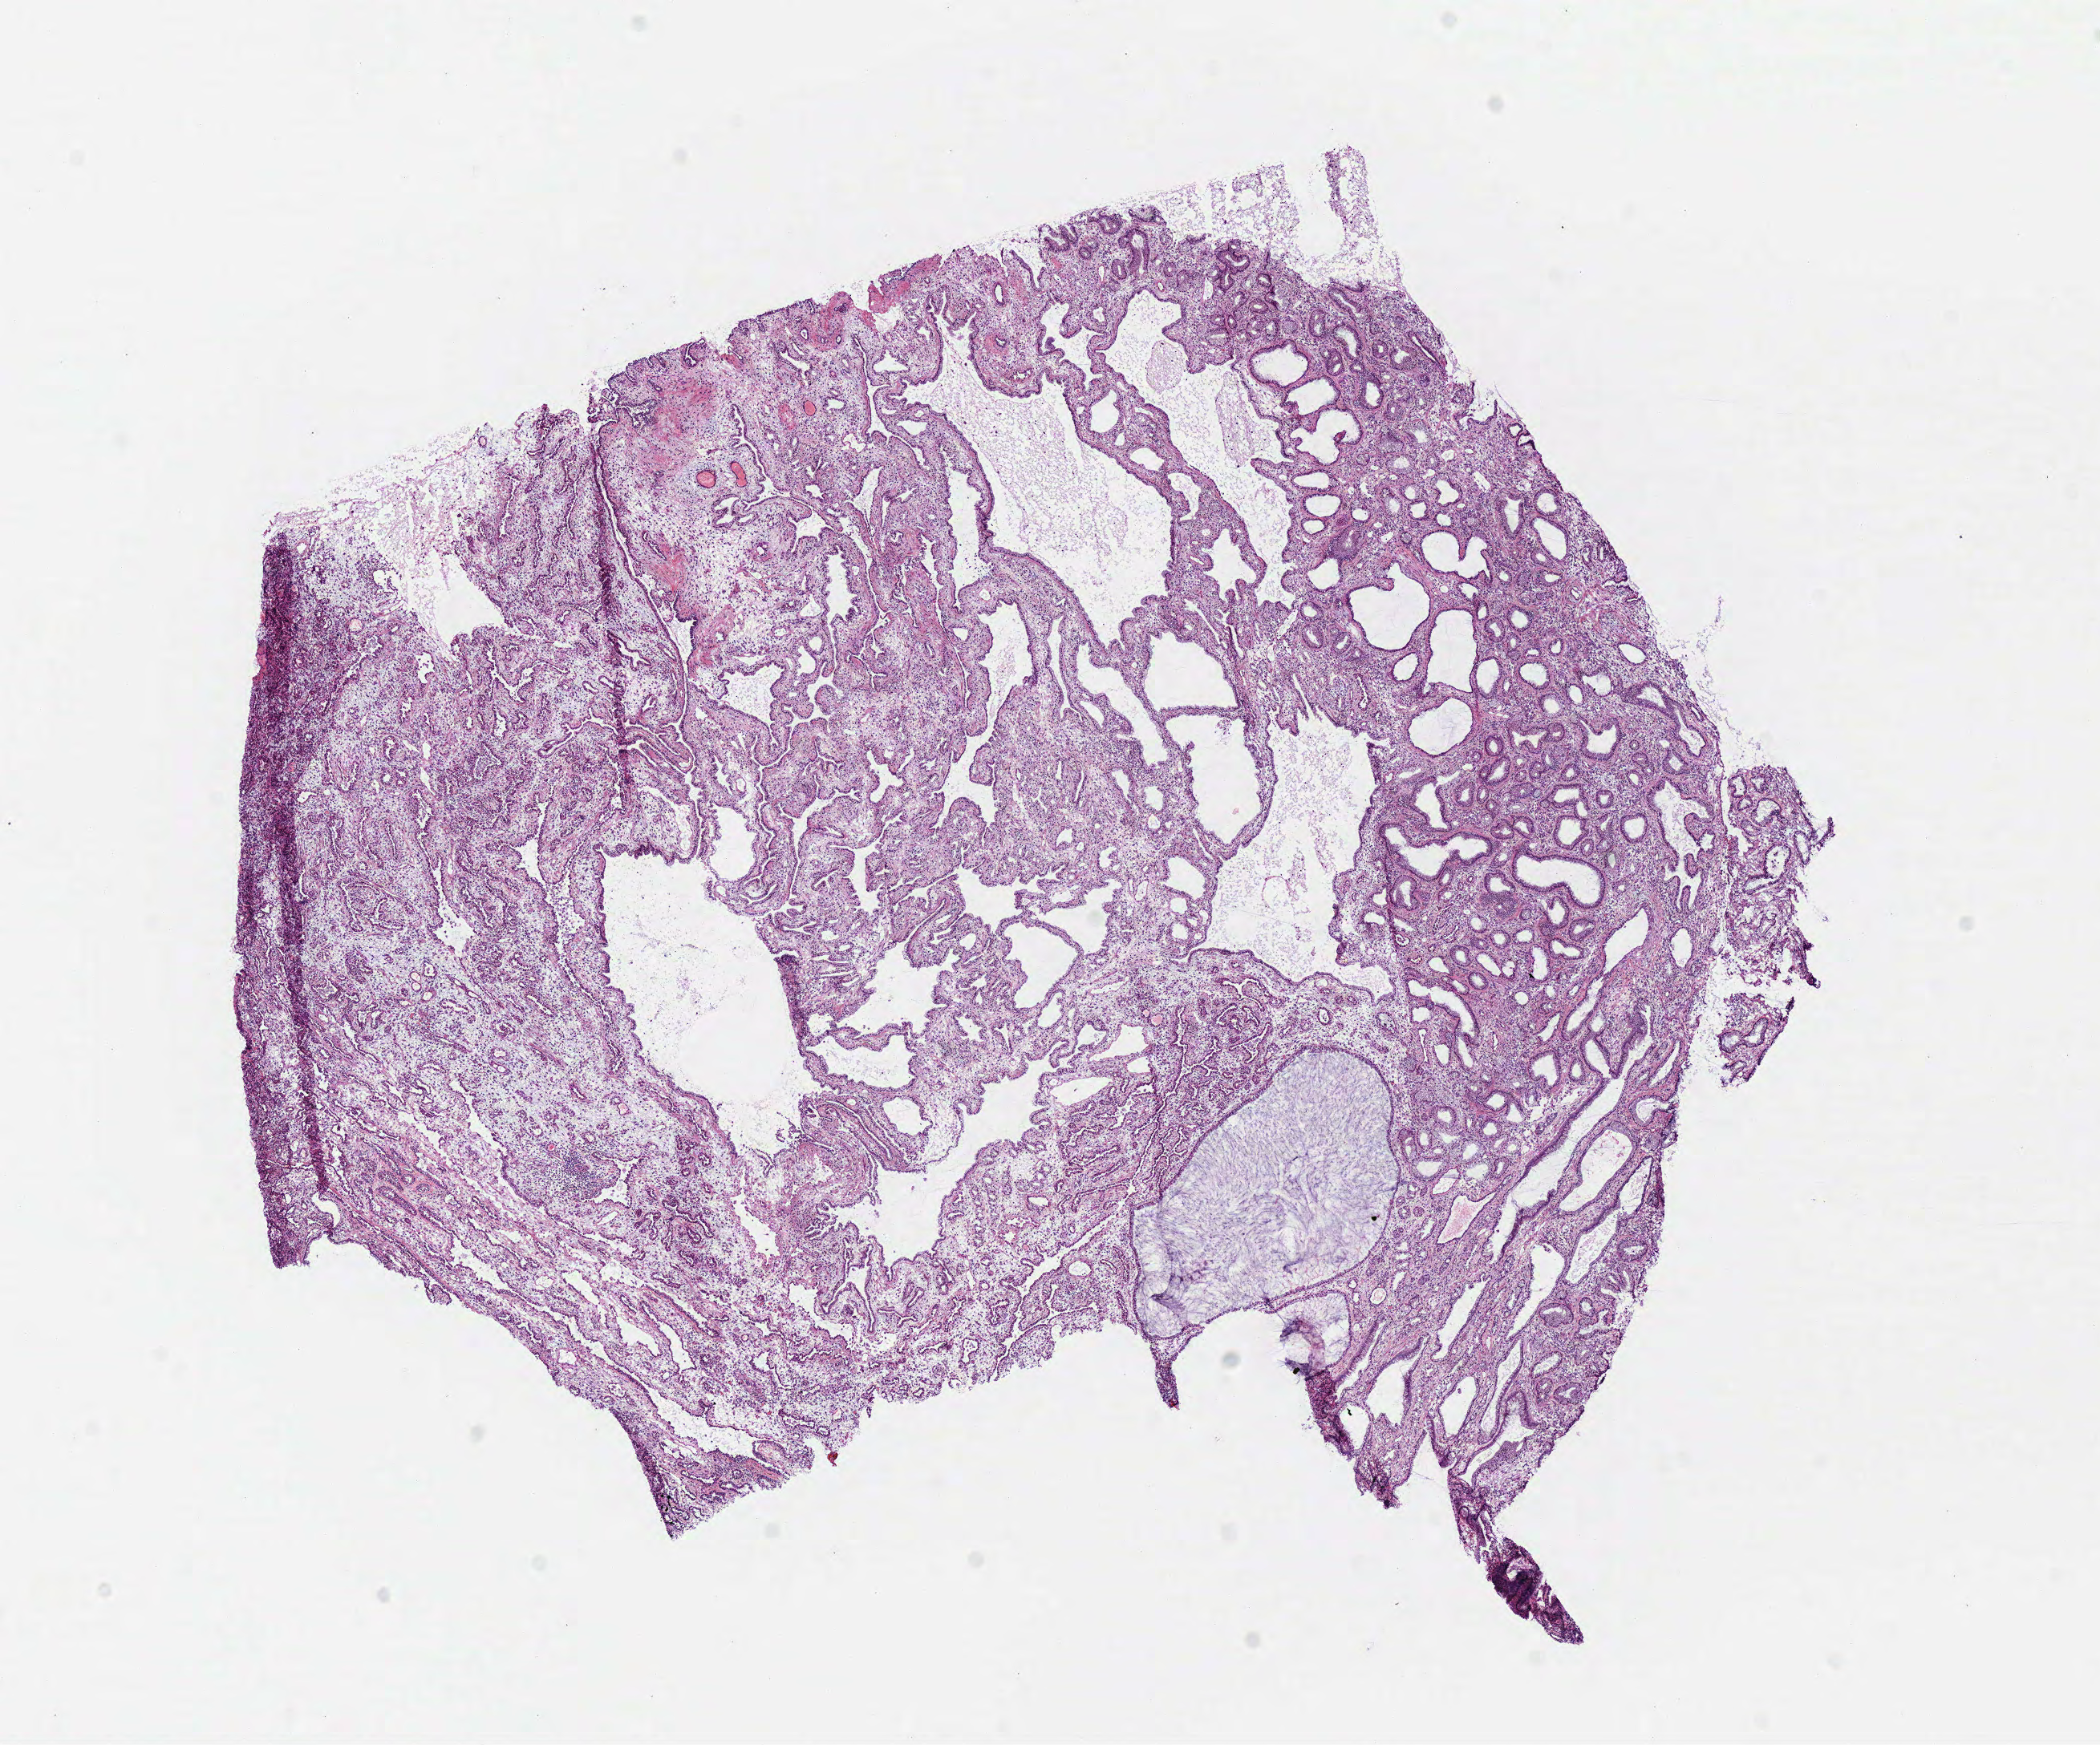
Digitized H&E tissue section (whole slide) — shown as a low-resolution overview of the whole scanned area (about 10.3 x 8.6 mm, slide scanned at 40x), frozen section, primary tumour sample from the lung. Male, age 60 years at initial diagnosis. Pathologist review of this section (percent, as recorded): tumour cells 100%, tumour nuclei 80%, normal cells 0%, stromal cells 0%, necrosis 0%. Infiltration values recorded for this section: lymphocyte infiltration 10%, monocyte infiltration 0%, neutrophil infiltration 0%.
• diagnosis: Mucinous adenocarcinoma (lower lobe, lung)
• laterality: left
• AJCC pathologic stage: IA (7th edition)